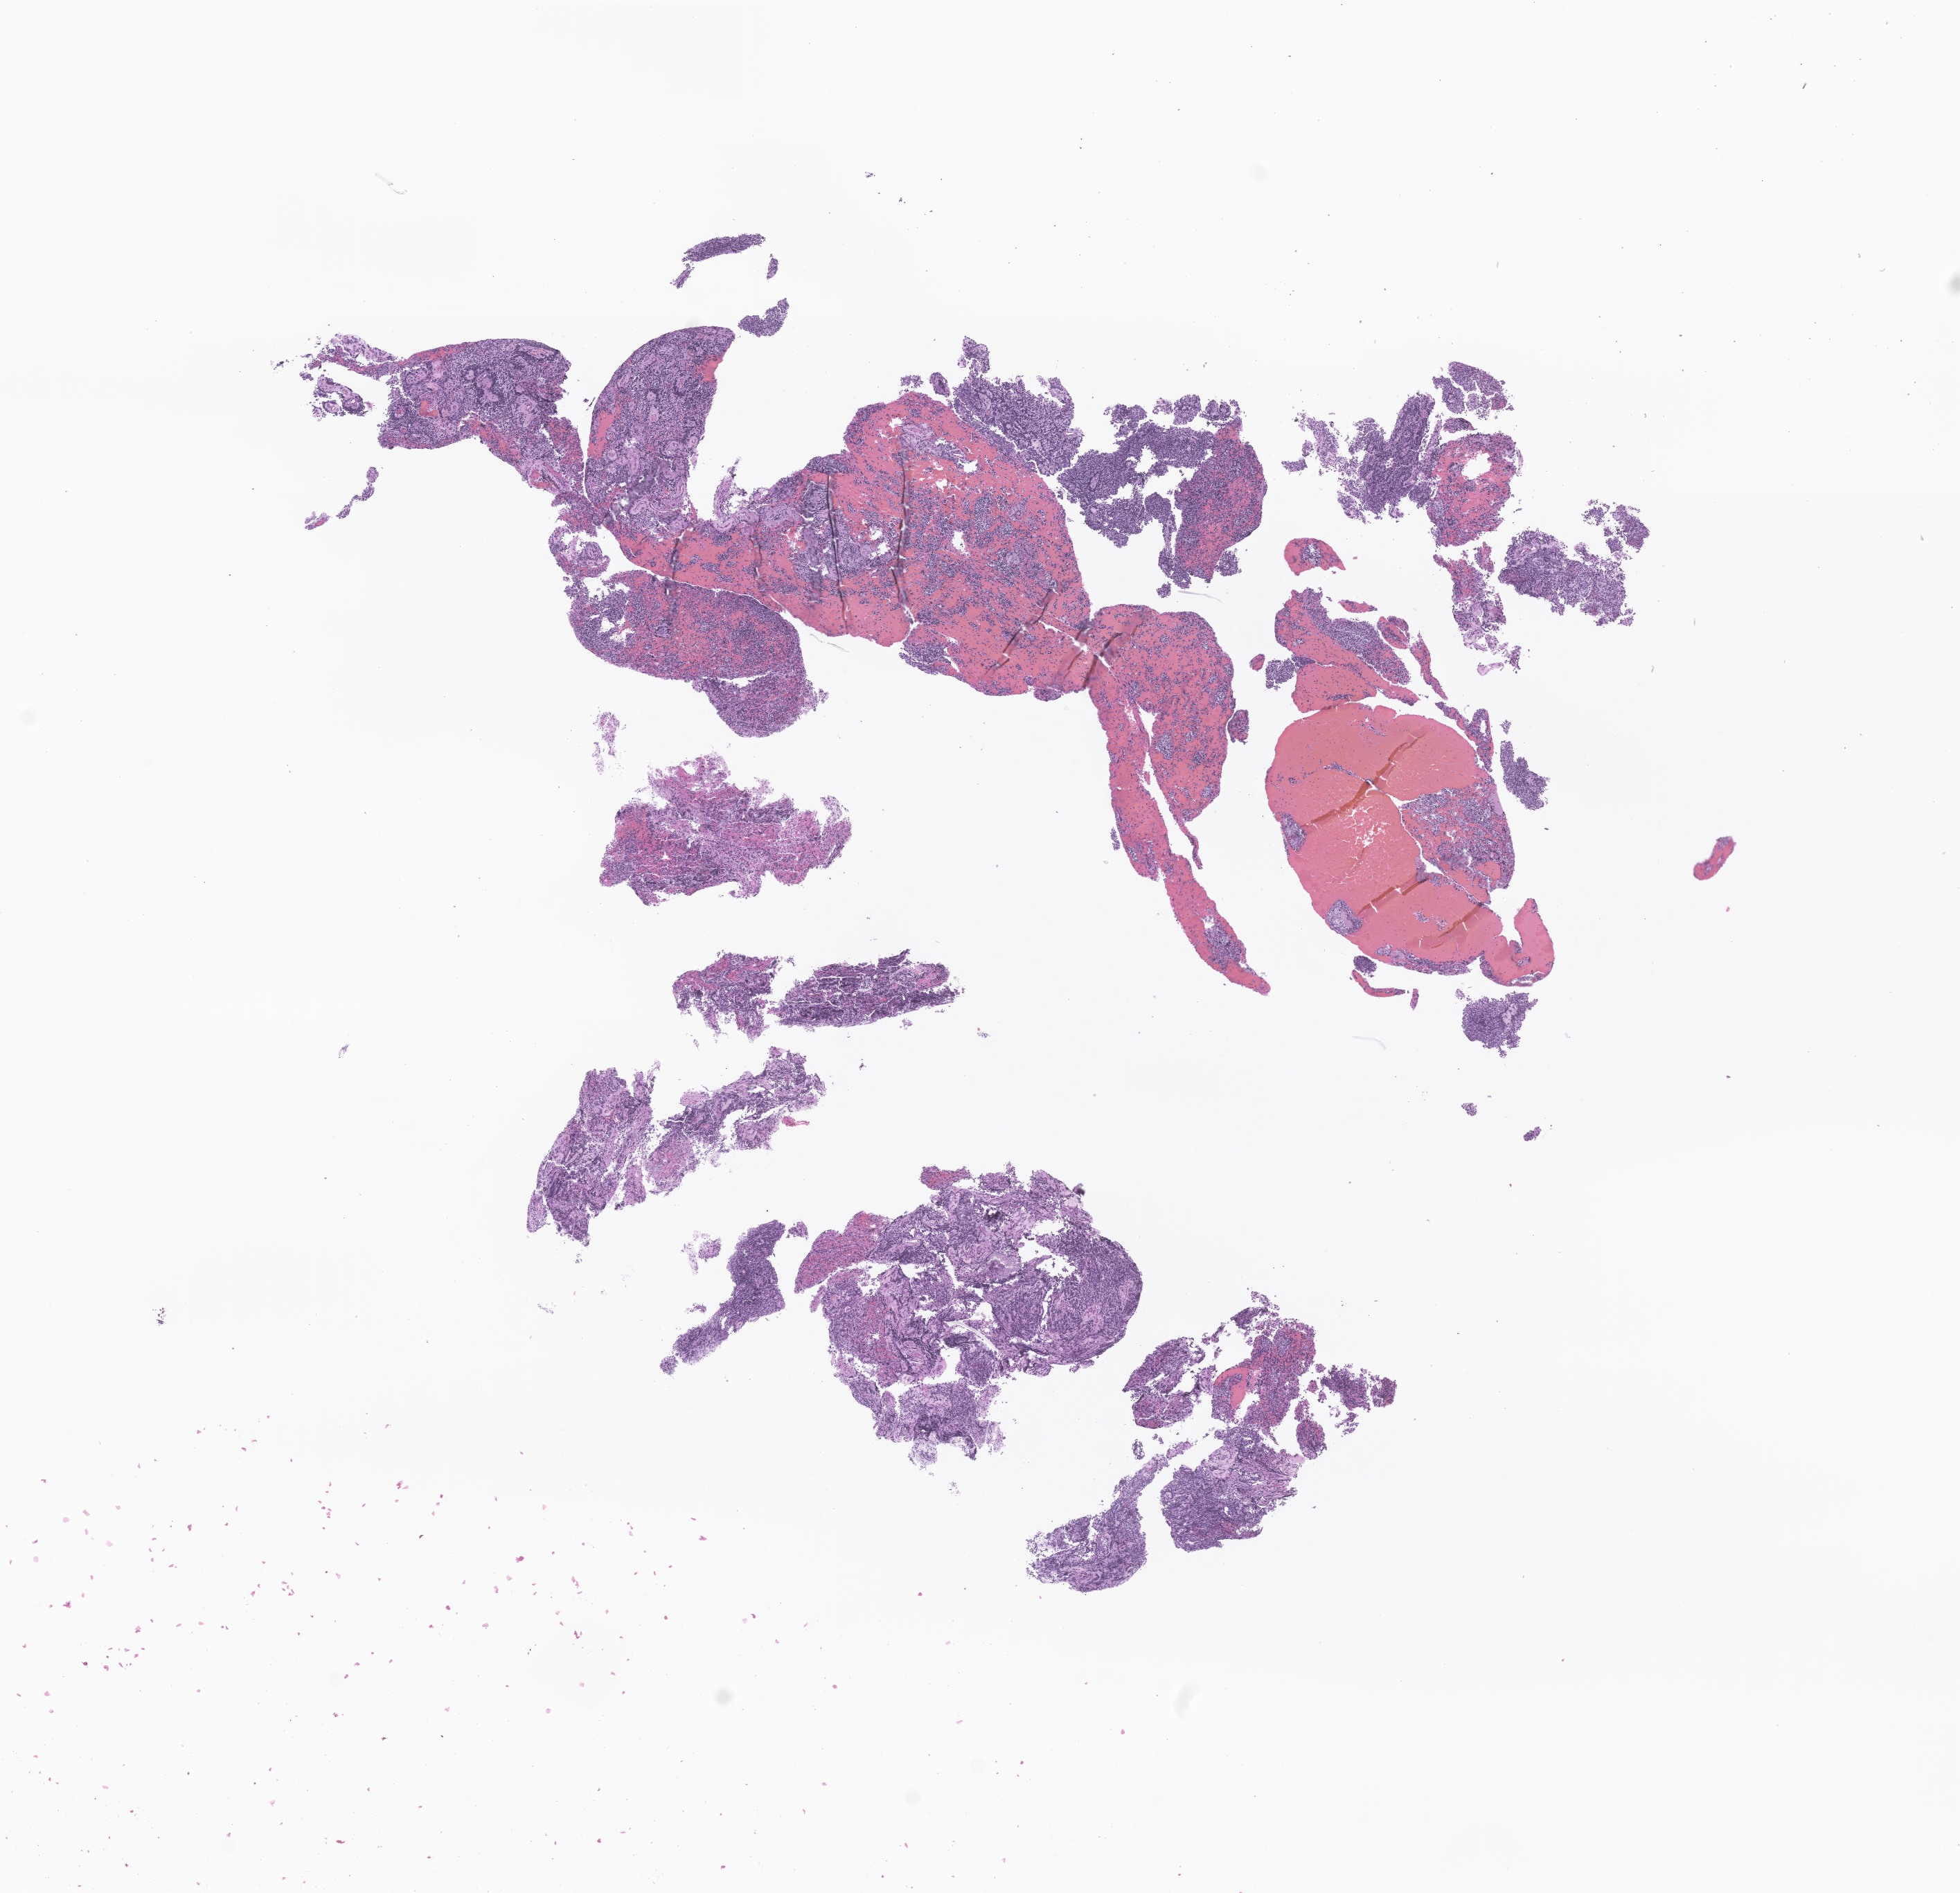
Digitized haematoxylin and eosin-stained section of tumor tissue from the brain, low-resolution overview of the scanned area, about 11.9 x 11.5 mm, FFPE section. Patient: female, age 43 months (3 years 7 months).
• recorded diagnosis: Neoplasm, malignant